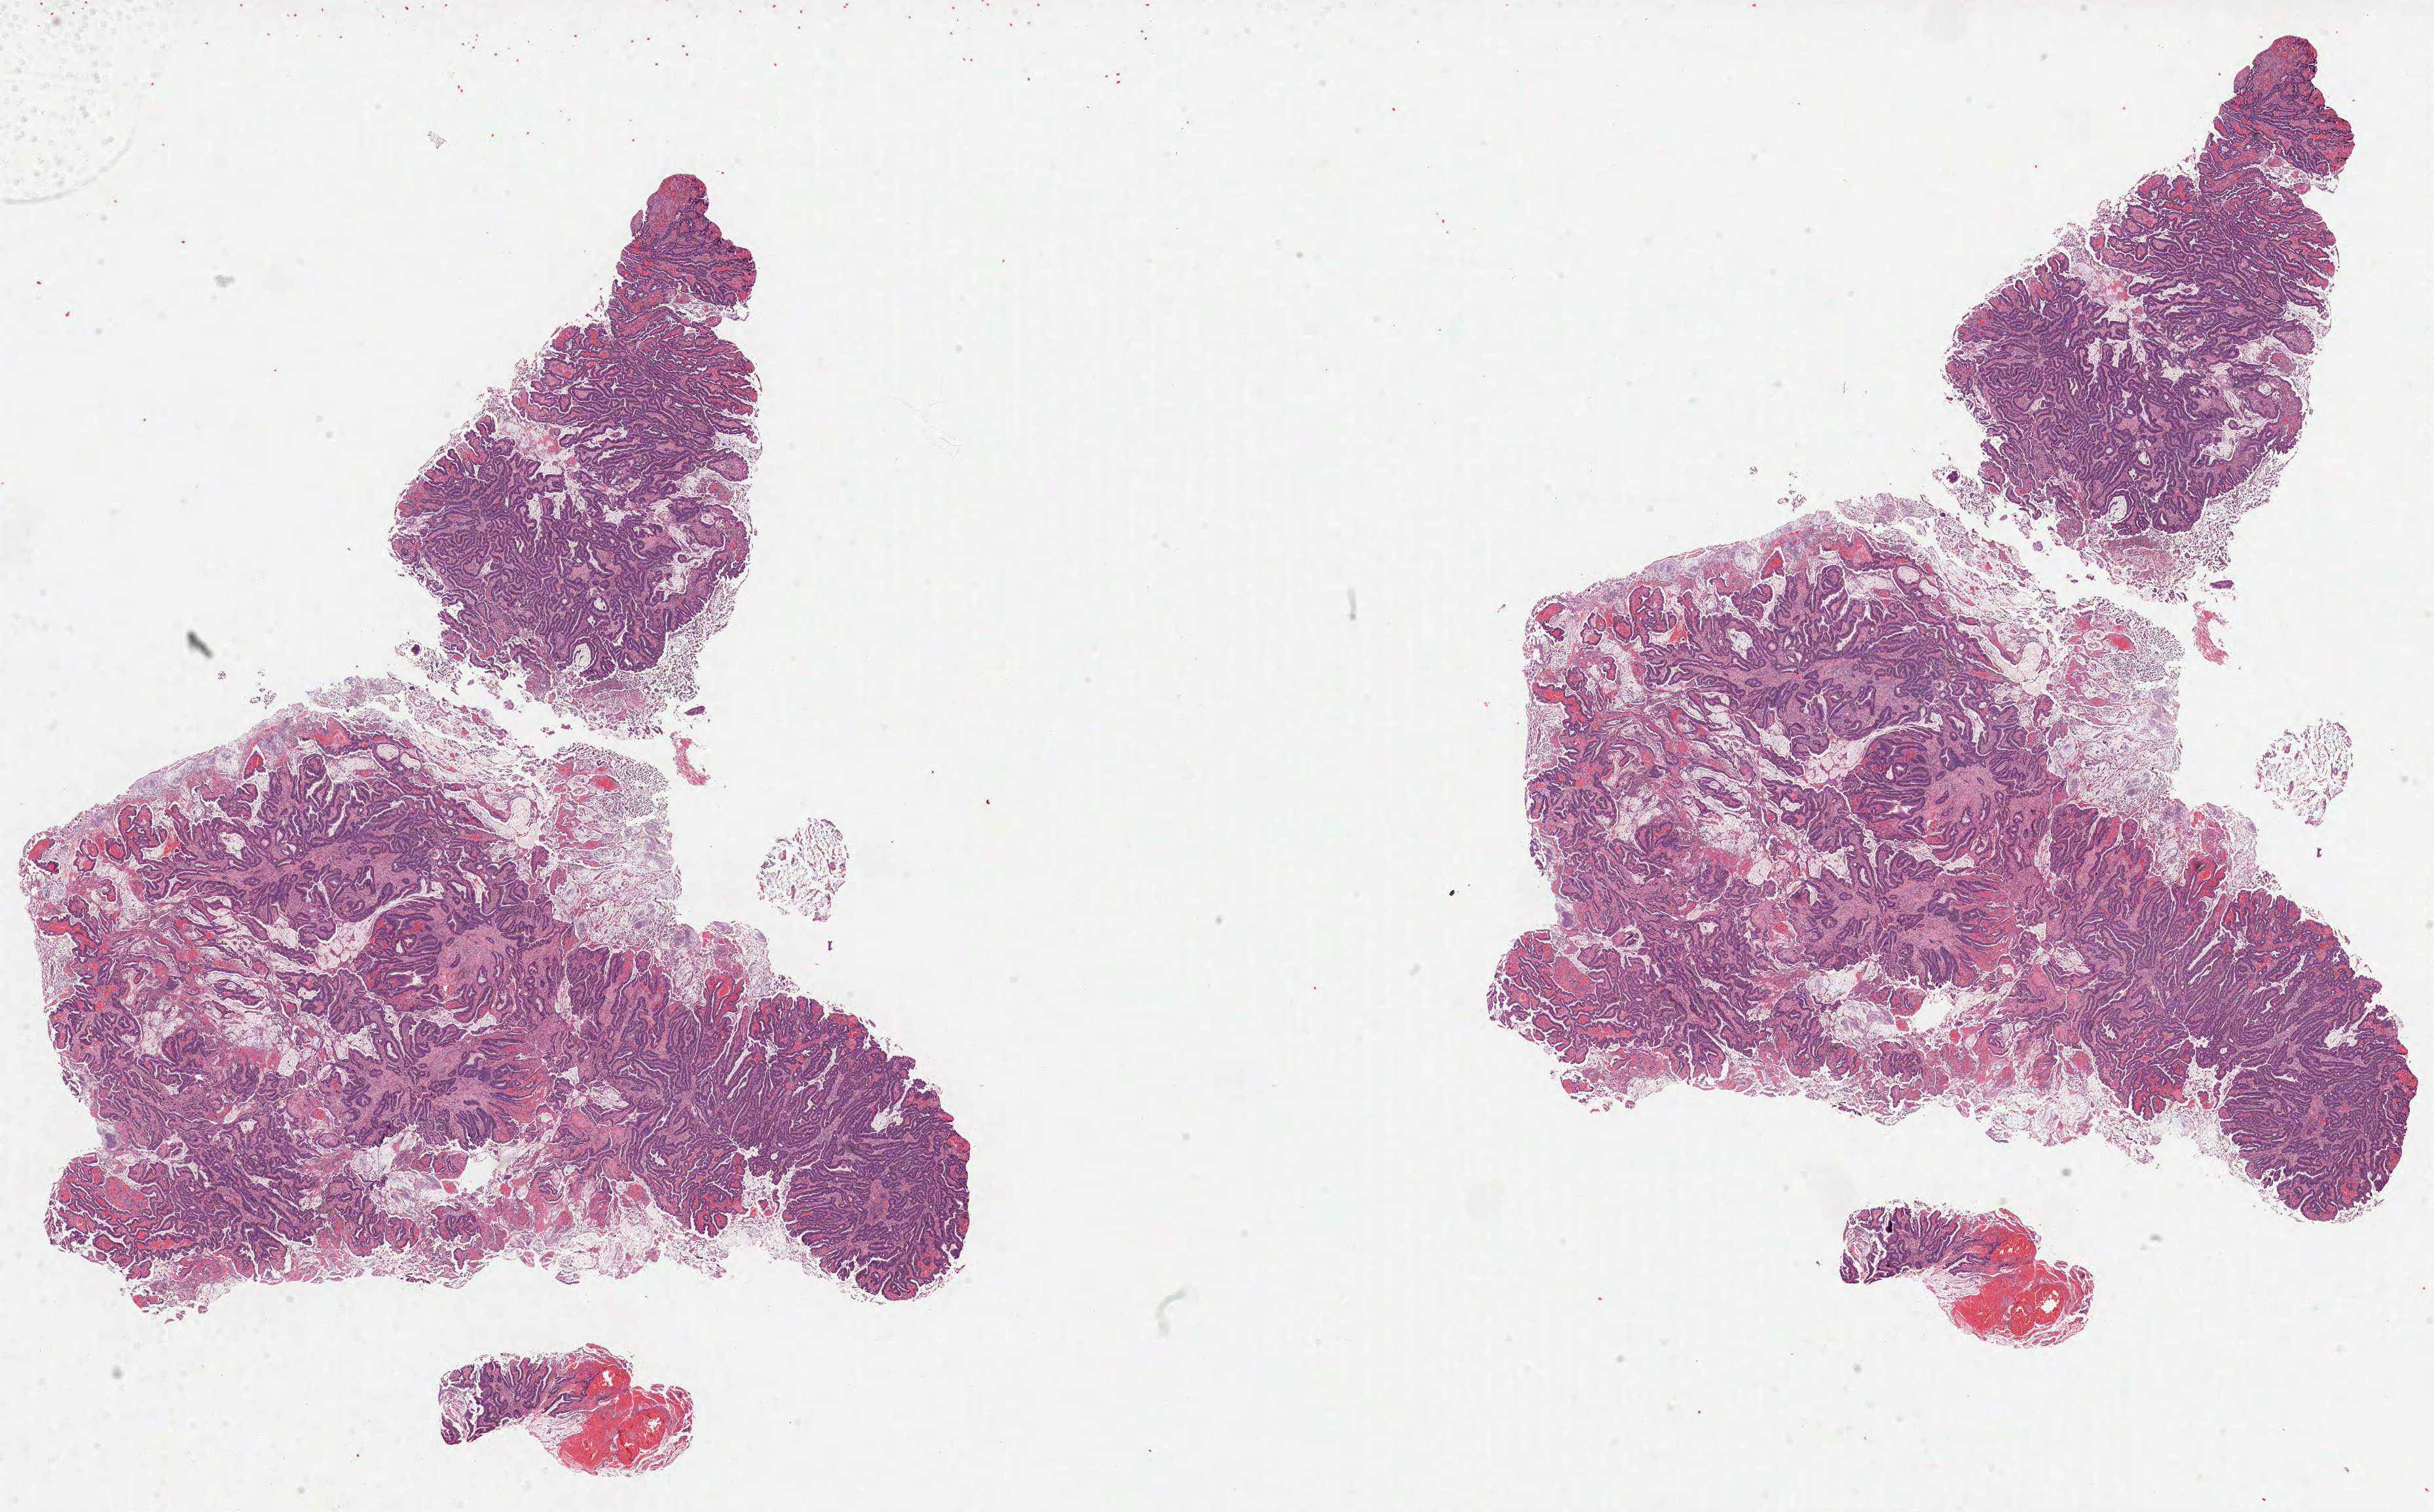
H&E whole-slide image — low-resolution overview of the scanned area, about 30.0 x 18.6 mm, formalin-fixed paraffin-embedded (FFPE) diagnostic section, primary tumour sample from the colon. Patient: male, age at initial diagnosis 60 years.
AJCC pathologic stage: IIA (7th edition). Lymph nodes positive (case pathology): 0 of 16 examined. Histologic diagnosis: Adenocarcinoma, NOS (ascending colon). TNM: T3 N0.